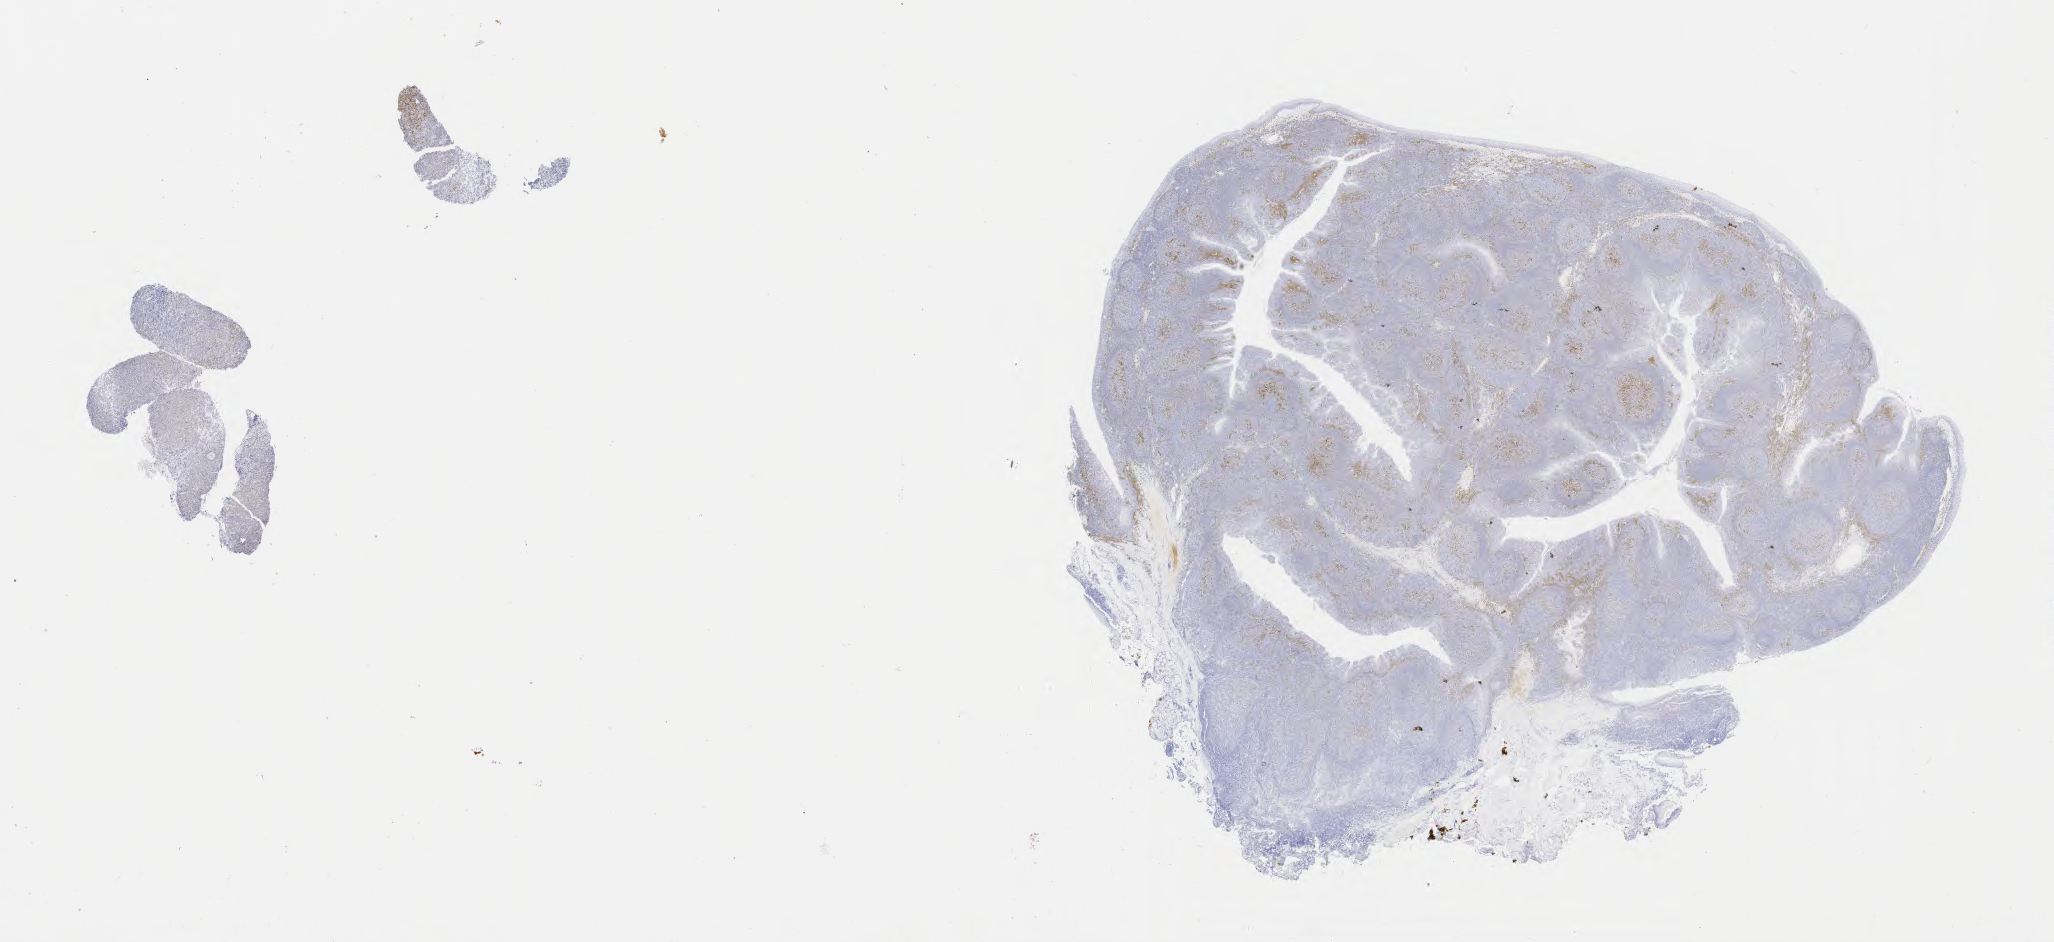
IHC for IRF4/MUM1, whole-slide image — whole scanned area (about 33.2 x 15.2 mm) shown as a low-resolution overview. Specimen: tumor tissue. Anatomic site: lymph node. Patient: male, age 54 years.
- diagnosis: Diffuse large B-cell lymphoma, NOS